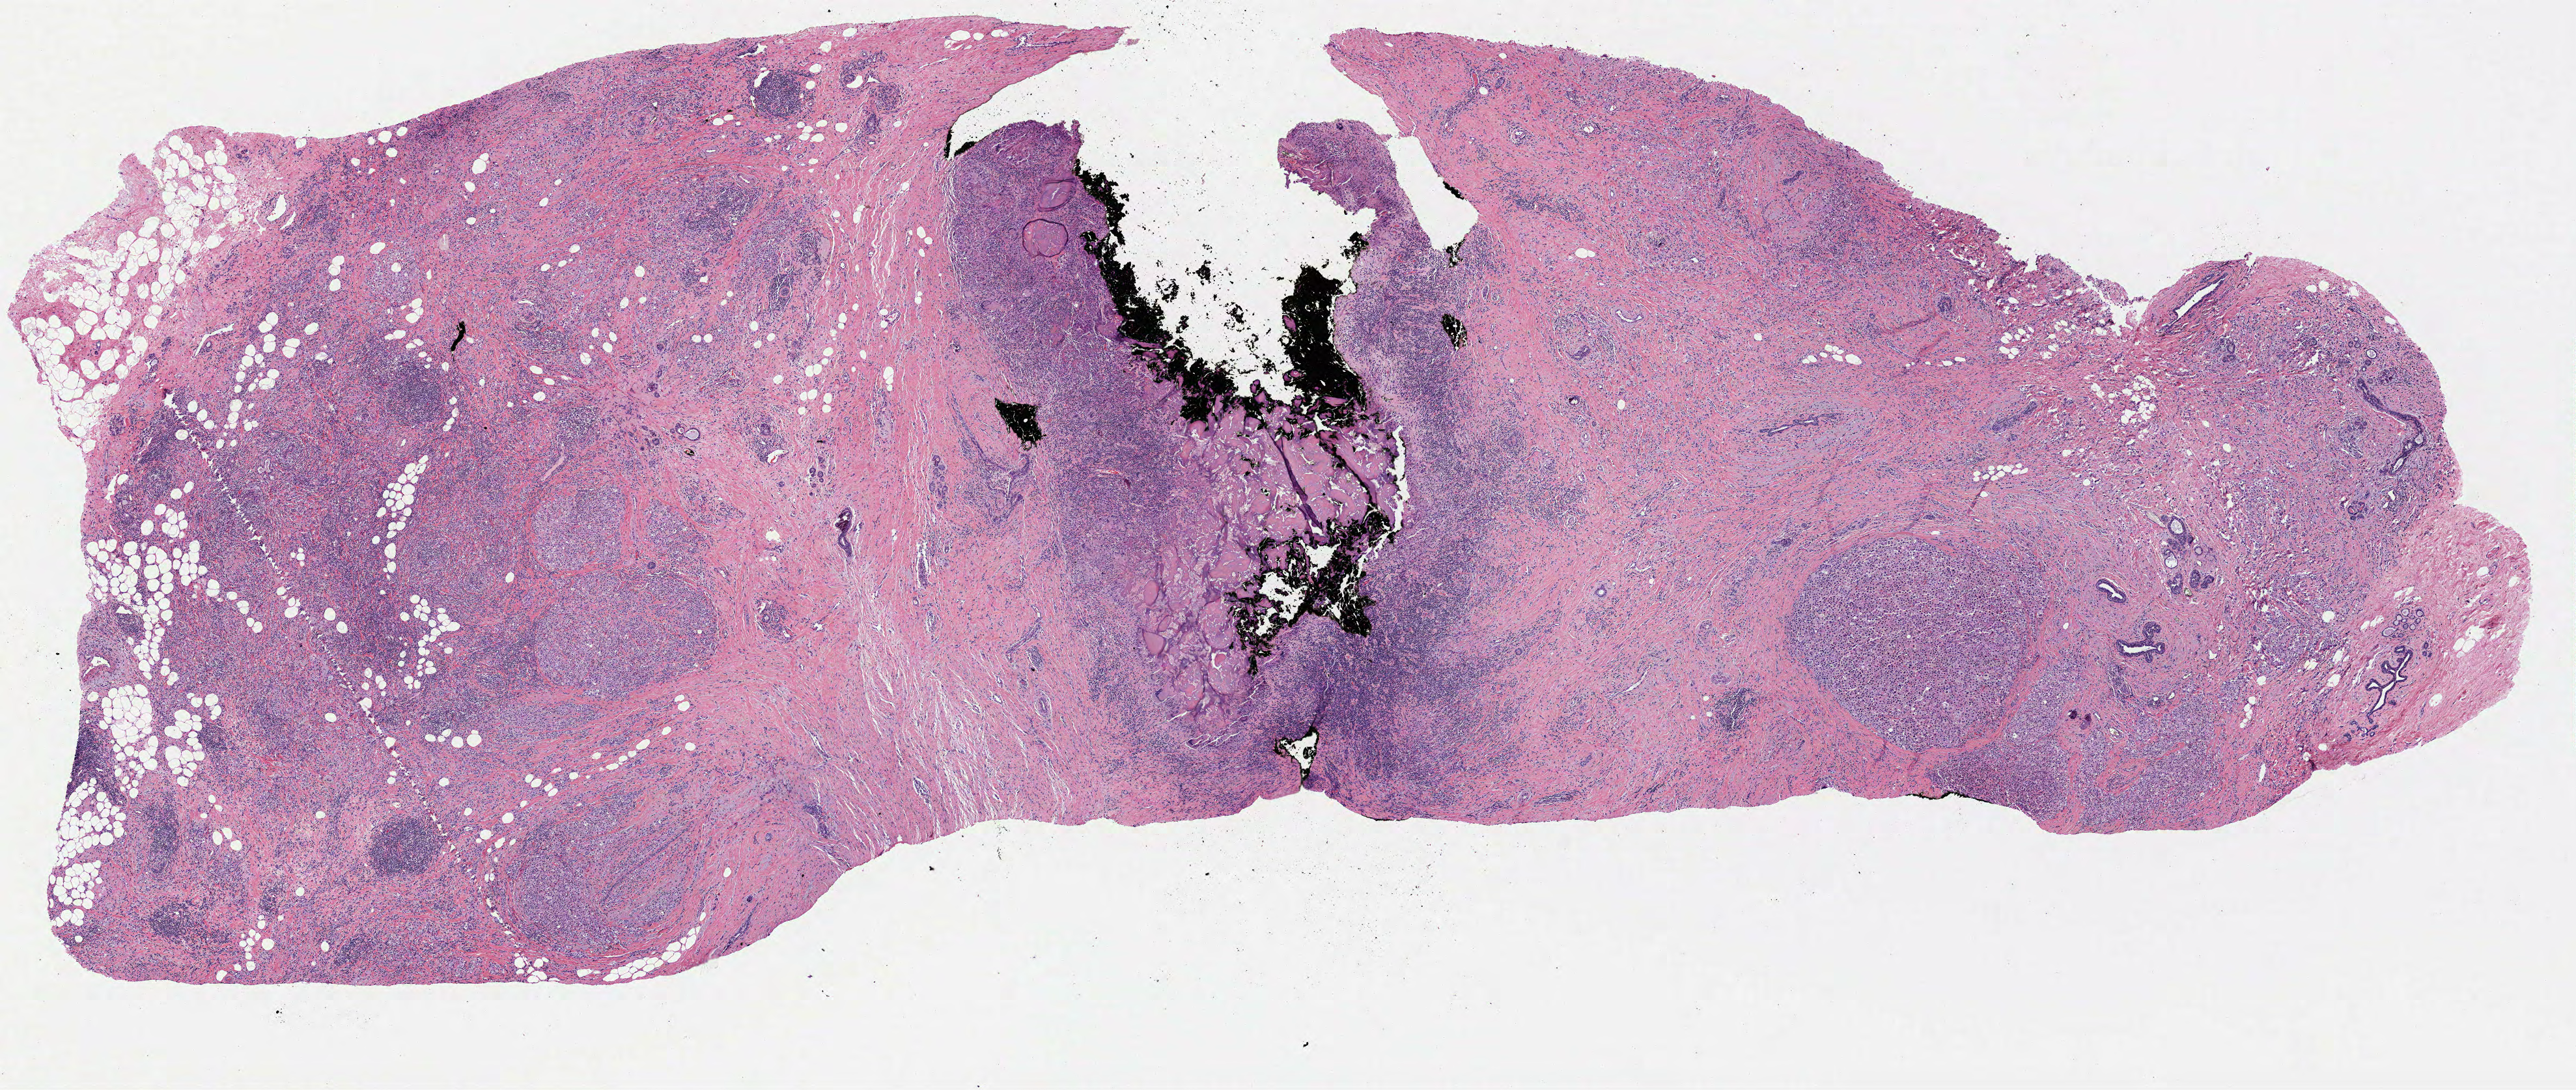
Whole-slide histology image, Hematoxylin and eosin (H&E) stained, shown as a low-resolution overview of the whole scanned area (about 16.0 x 6.8 mm, from a 40x scan); formalin-fixed paraffin-embedded (FFPE) diagnostic section; primary tumour sample from the breast. Female, age 65 years at initial diagnosis.
AJCC pathologic stage: IIA. Pathologic diagnosis: Lobular carcinoma, NOS. Laterality: left.